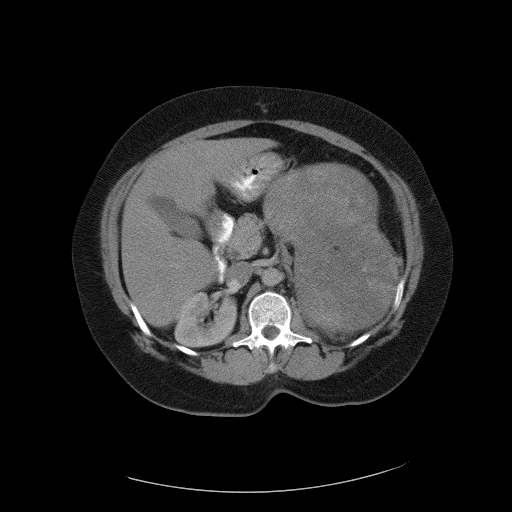
Contrast-enhanced abdominal CT, one axial slice. Slice 64 of 90 in the series (ordered by position). 120 kVp. Intravenous contrast given. Soft-tissue window (W 400 / L 40 HU). 5 mm slice thickness. 512 × 512 image matrix, field of view 480 × 480 mm. Patient: female, 55 years. From the clinical record (not read from this slice): diagnosis: adrenocortical carcinoma; tumour side: left adrenal; tumour size at pathology: 22 cm; Ki-67 index: 10 %; stage (as recorded): 3.
Annotated regions visible in this slice (semi-automatically segmented with operator editing):
- mass: bounding box <267,162,396,332> (left, top, right, bottom; pixels)